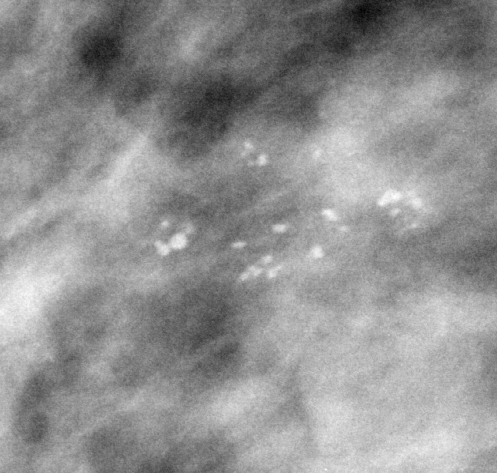
Region of interest cut from a scanned film mammogram (one marked finding), right breast, MLO view, BI-RADS breast density category 3 (scale 1–4).
Marked abnormality: calcifications, morphology pleomorphic, distribution clustered; BI-RADS assessment category 4; pathology (as recorded): benign.